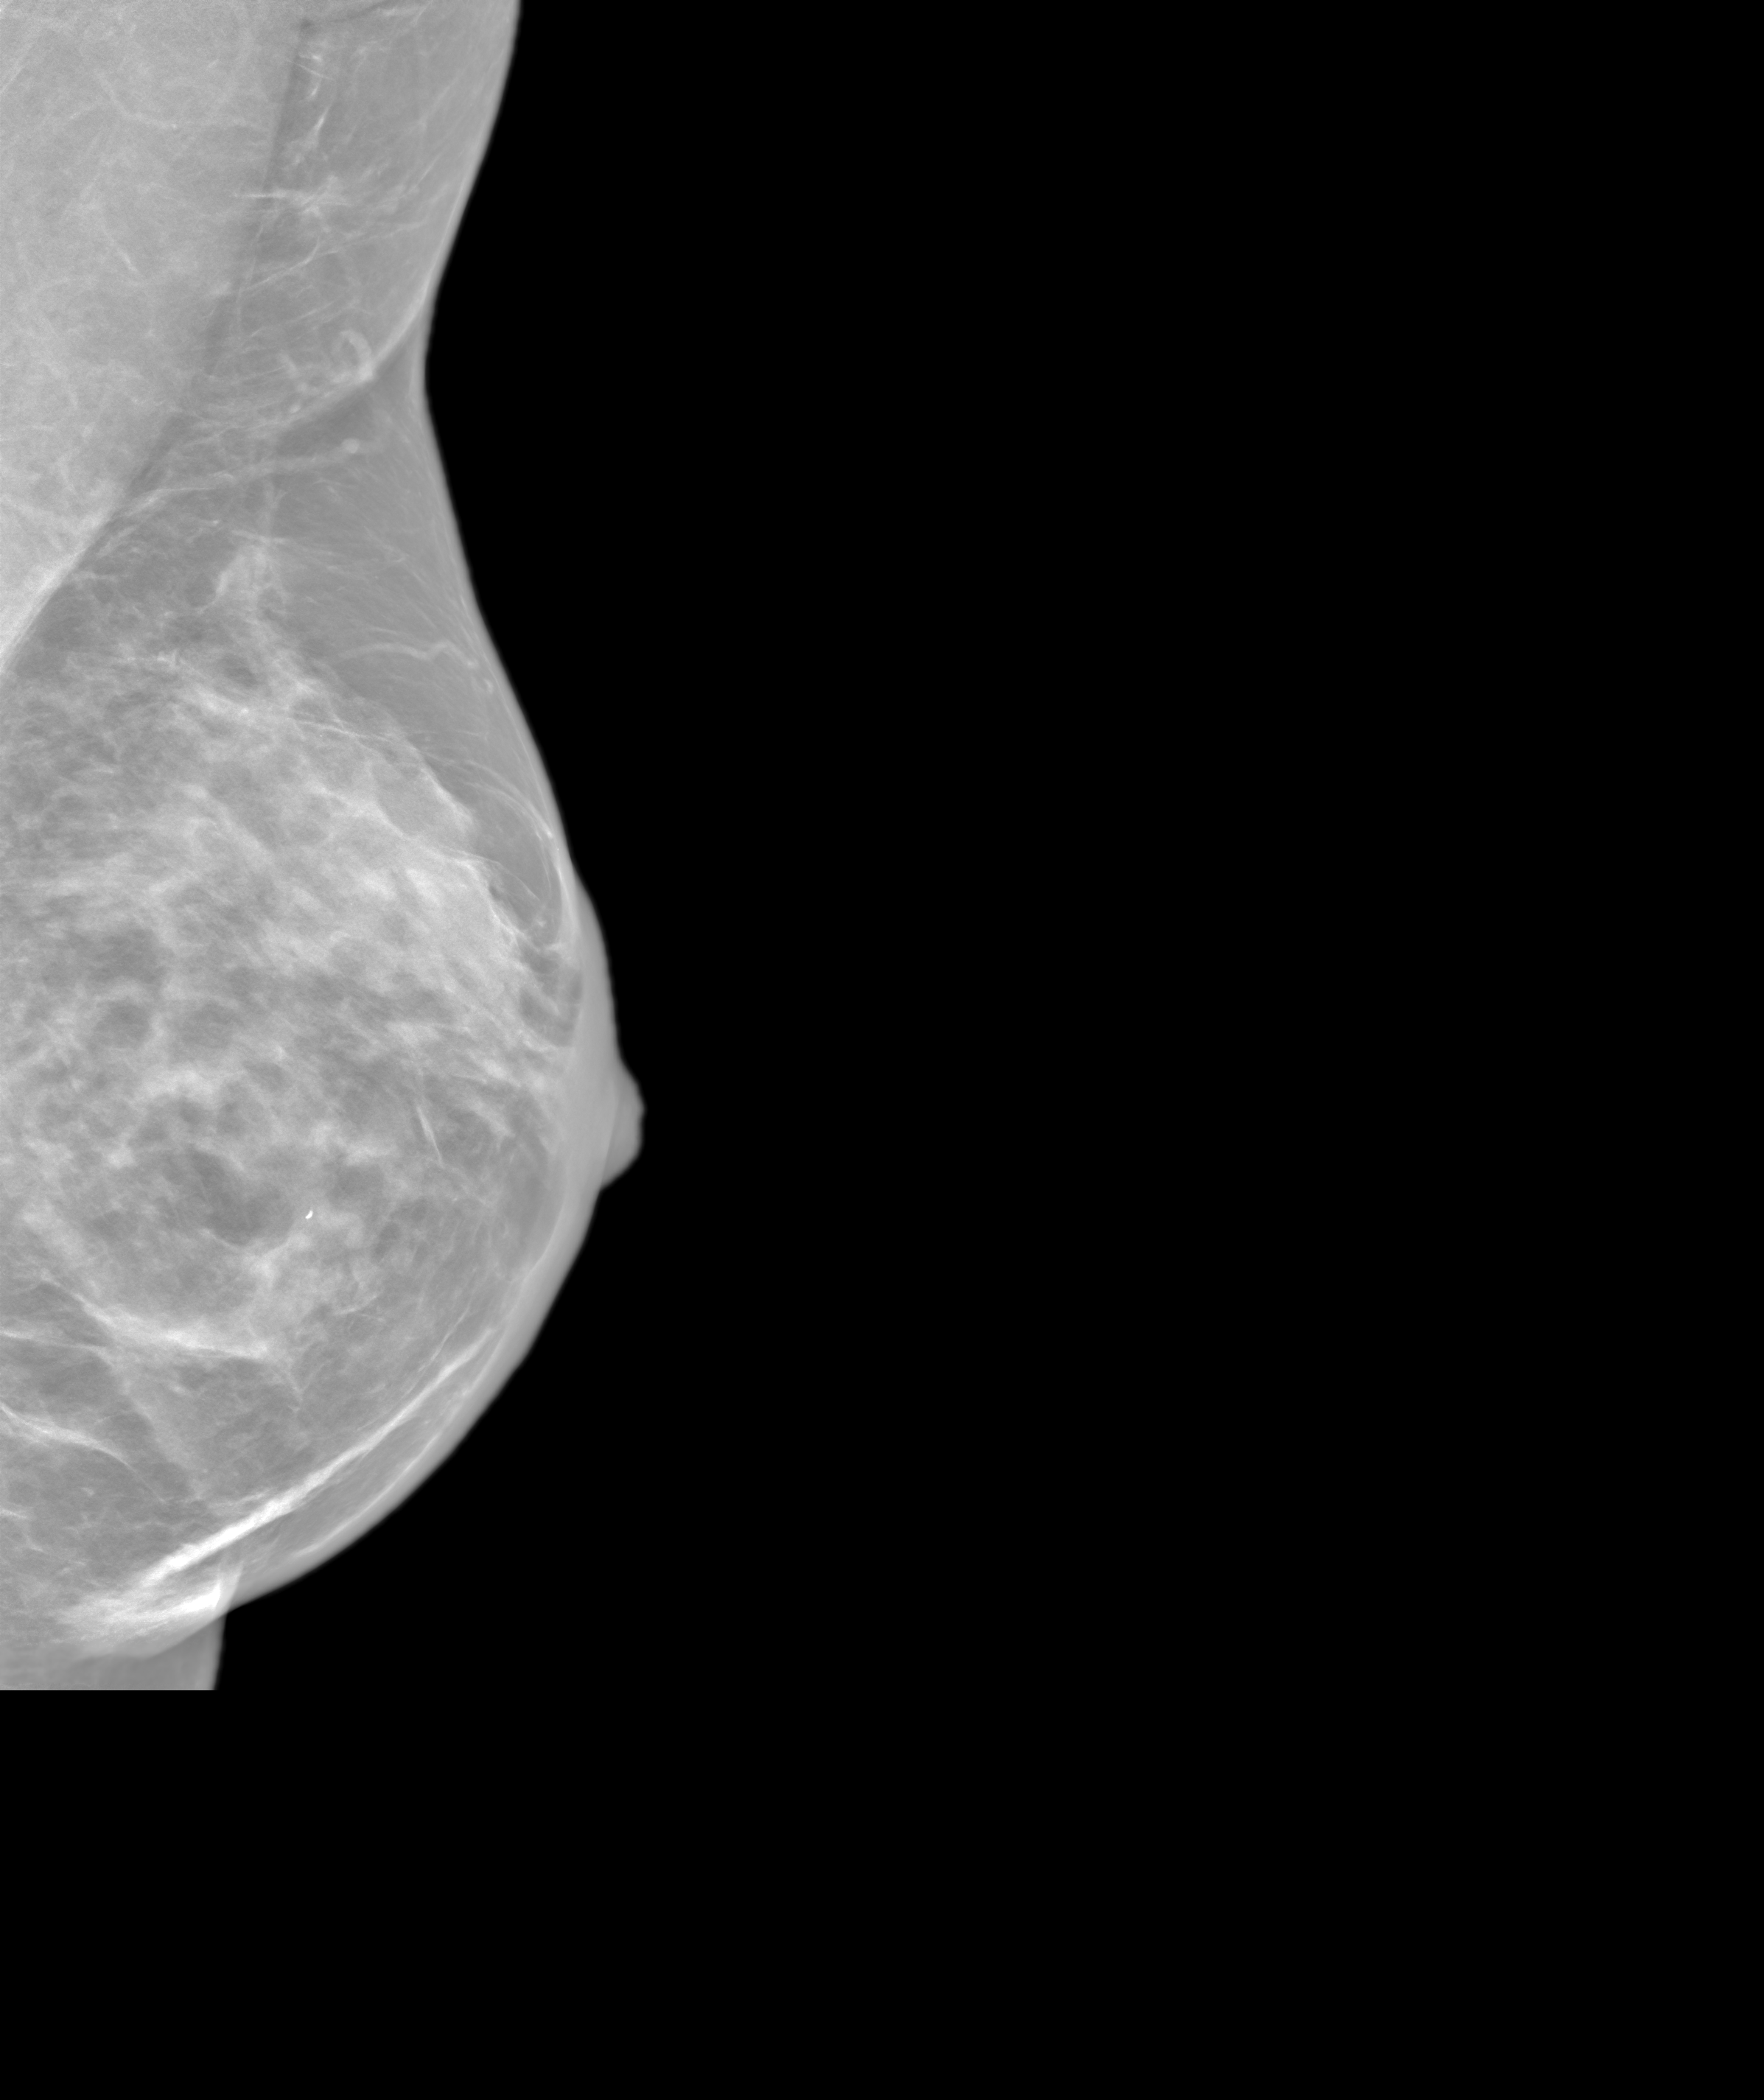
Annual screening mammography examination, system: SenoIris_1SP1.2(425). Patient aged 43 years (female).
Image type: synthesized 2-D view from tomosynthesis. Breast: left. Projection: MLO view.